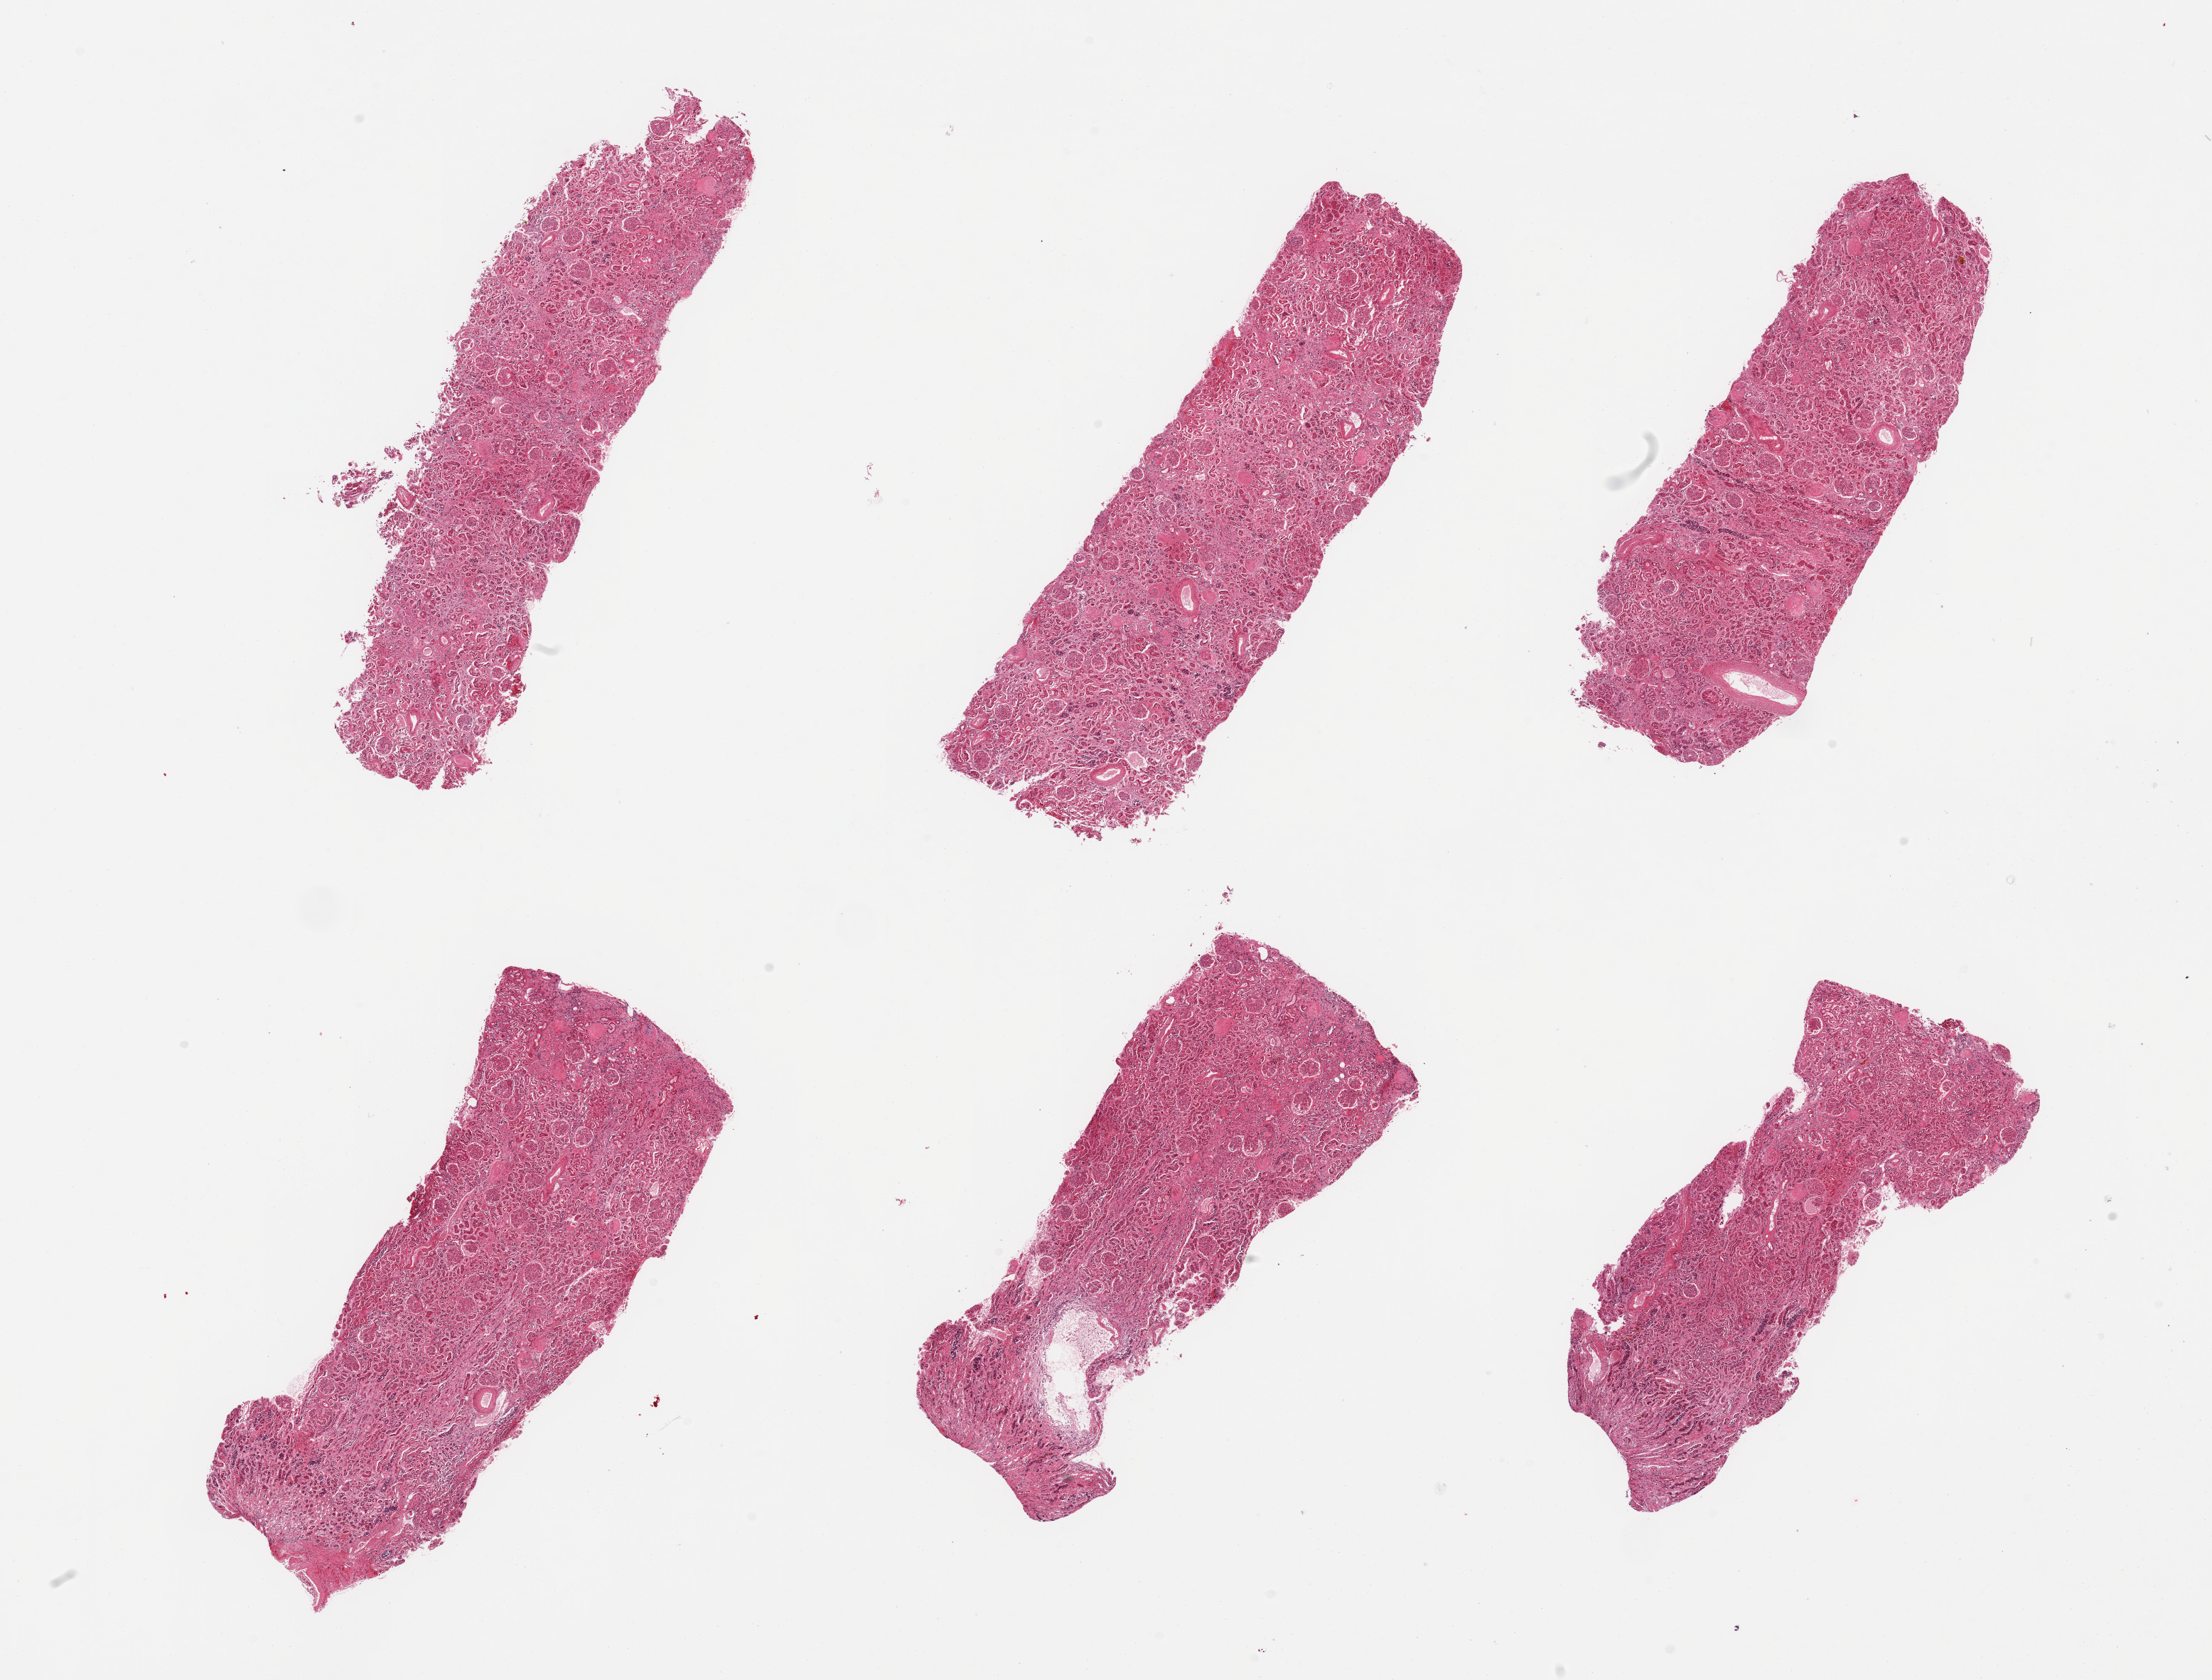
Digitized hematoxylin and eosin (H&E)-stained section, brightfield — whole scanned area (about 24.6 x 18.7 mm) shown as a low-resolution overview; PAXgene-fixed paraffin-embedded (PFPE) section; target tissue: renal cortex; donor tissue sample. Donor sex: female.
Reviewer comment on this tissue sample: 6 pieces; glomeruli in all sections, several sclerotic, arteriosclerosis, small portion of medulla.